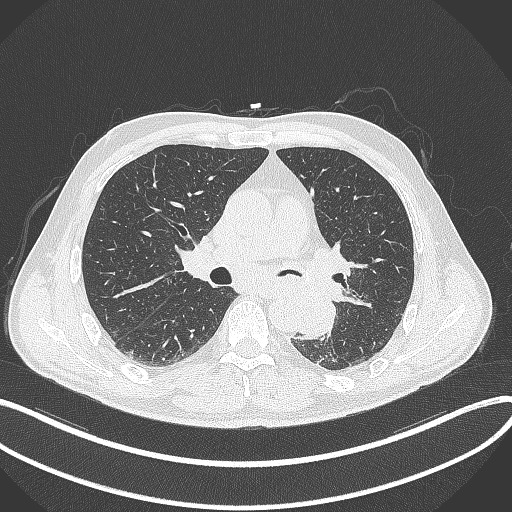
Chest CT, one axial slice; slice 198 of 329 in the series (ordered by position); 120 kVp; lung window (W 1500 / L -600 HU); 512 × 512 image matrix. Patient: male, 59 years. Case-level facts recorded for this patient, not image findings: clinical TNM (as recorded): T2a N2 M0.
Structures marked on this image (rectangle marked by the reading radiologist):
- lung tumour (recorded histology: squamous cell carcinoma): bounding box [x1, y1, x2, y2] px = [296, 290, 338, 342]